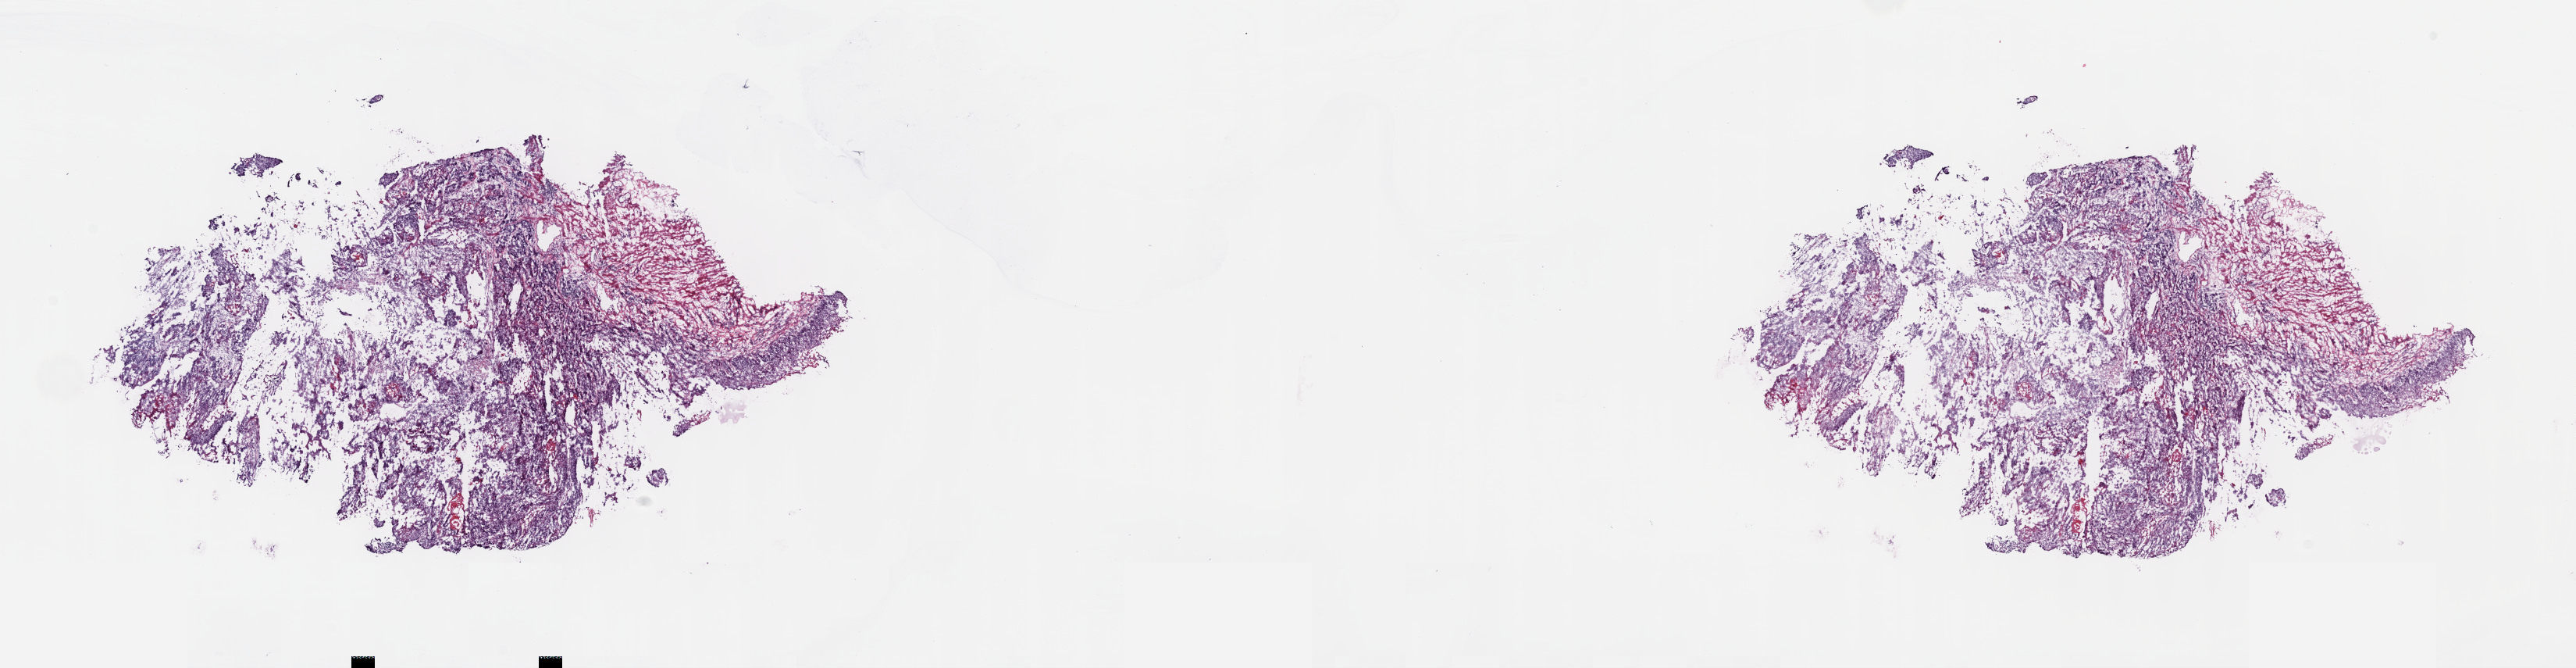
Digitized H&E-stained tissue section (whole slide) — a low-resolution overview of the entire scanned area, about 26.7 x 6.9 mm. Frozen section. Primary tumour sample from the esophagus. Female patient; age at initial diagnosis 70 years. Histologic grade: GX (grade cannot be assessed). Pathologist review of this section (percent, as recorded): tumour cells 100%, tumour nuclei 75%, normal cells 0%, stromal cells 0%, necrosis 0%. Inflammatory infiltration, as recorded: lymphocyte infiltration 5%, monocyte infiltration 0%, neutrophil infiltration 0%.
AJCC pathologic stage: IIA (6th edition). Diagnosis: Squamous cell carcinoma, NOS (middle third of esophagus). Lymph nodes positive (case pathology): 2 of 8 examined.